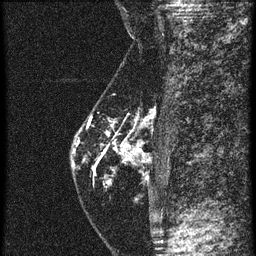
Breast MRI (dynamic contrast-enhanced), one sagittal slice; position 20 of 60 along the scan axis; 4 images stored at this slice position (order not interpretable as contrast timing); 1.5 T; TE 4.2 ms, TR 20.4 ms; 256 × 256 image matrix. Female patient, age 46 years. Case-level facts recorded for this patient, not image findings: setting: breast cancer imaged before/during neoadjuvant chemotherapy; receptor status: triple-negative.
Annotated regions visible in this slice (semi-automatically segmented with operator editing):
- analysis volume of interest (the breast-tissue region the enhancement analysis was run in; not a lesion): bounding box <71,82,145,201> (left, top, right, bottom; pixels)
- tumour enhancement mask (voxels above the 90 % enhancement threshold inside the analysis volume of interest): <108,134,129,185>